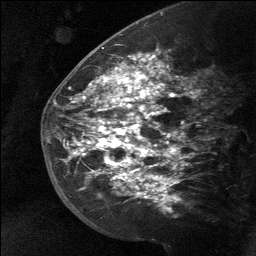
Breast MRI (dynamic contrast-enhanced), one sagittal slice; dynamic contrast-enhanced study with each time point stored as its own series, time point 2 of 3 at this slice position (early post-contrast, ordered by acquisition time); 1.5 T; TE 4.8 ms, TR 27 ms; 256 × 256 image matrix. Female patient, age 39 years. Case-level facts recorded for this patient, not image findings: setting: breast cancer imaged before/during neoadjuvant chemotherapy; receptor status: HER2-positive.
Structures marked on this image (semi-automatic segmentation, software-assisted and operator-edited):
- analysis volume of interest (the breast-tissue region the enhancement analysis was run in; not a lesion): bounding box [x1, y1, x2, y2] px = [58, 40, 183, 217]
- tumour enhancement mask (voxels above the 90 % enhancement threshold inside the analysis volume of interest): [68, 53, 169, 199]